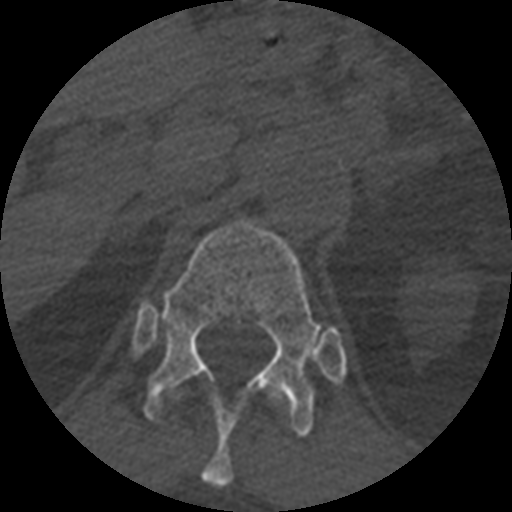
CT including the spine, one axial slice; position 392 of 399 along the scan axis; reconstruction kernel STANDARD; bone window (W 1800 / L 400 HU); 1.25 mm slice thickness; 512 × 512 image matrix. Patient age 71 years. Case-level facts recorded for this patient, not image findings: primary cancer: prostate.
Outlined on this slice (semi-automatically segmented with operator editing):
- T11 vertebra: bounding box <203,392,290,488> (left, top, right, bottom; pixels)
- T12 vertebra: <144,220,323,436>